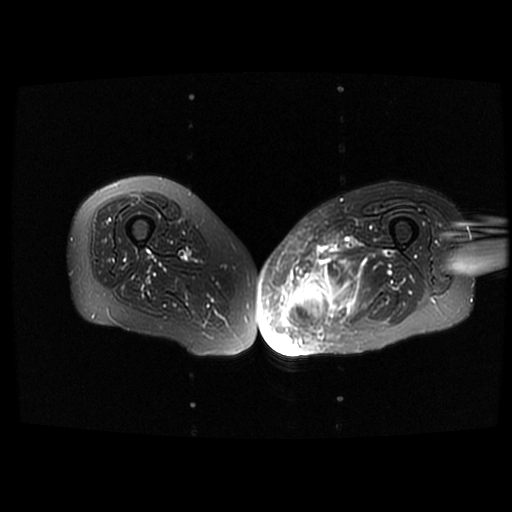
MRI of an extremity soft-tissue mass, one axial slice. Position 38 of 42 along the scan axis. T2-weighted fat-saturated. 512 × 512 image matrix, field of view 420 × 420 mm. Female patient. From the clinical record (not read from this slice): histological type: pleomorphic leiomyosarcoma; grade: high; site of the primary tumour: left thigh.
Outlined on this slice (manually delineated by an expert):
- gross tumour volume including surrounding oedema: bounding box (x1, y1, x2, y2) in pixels: (282, 259, 354, 328)